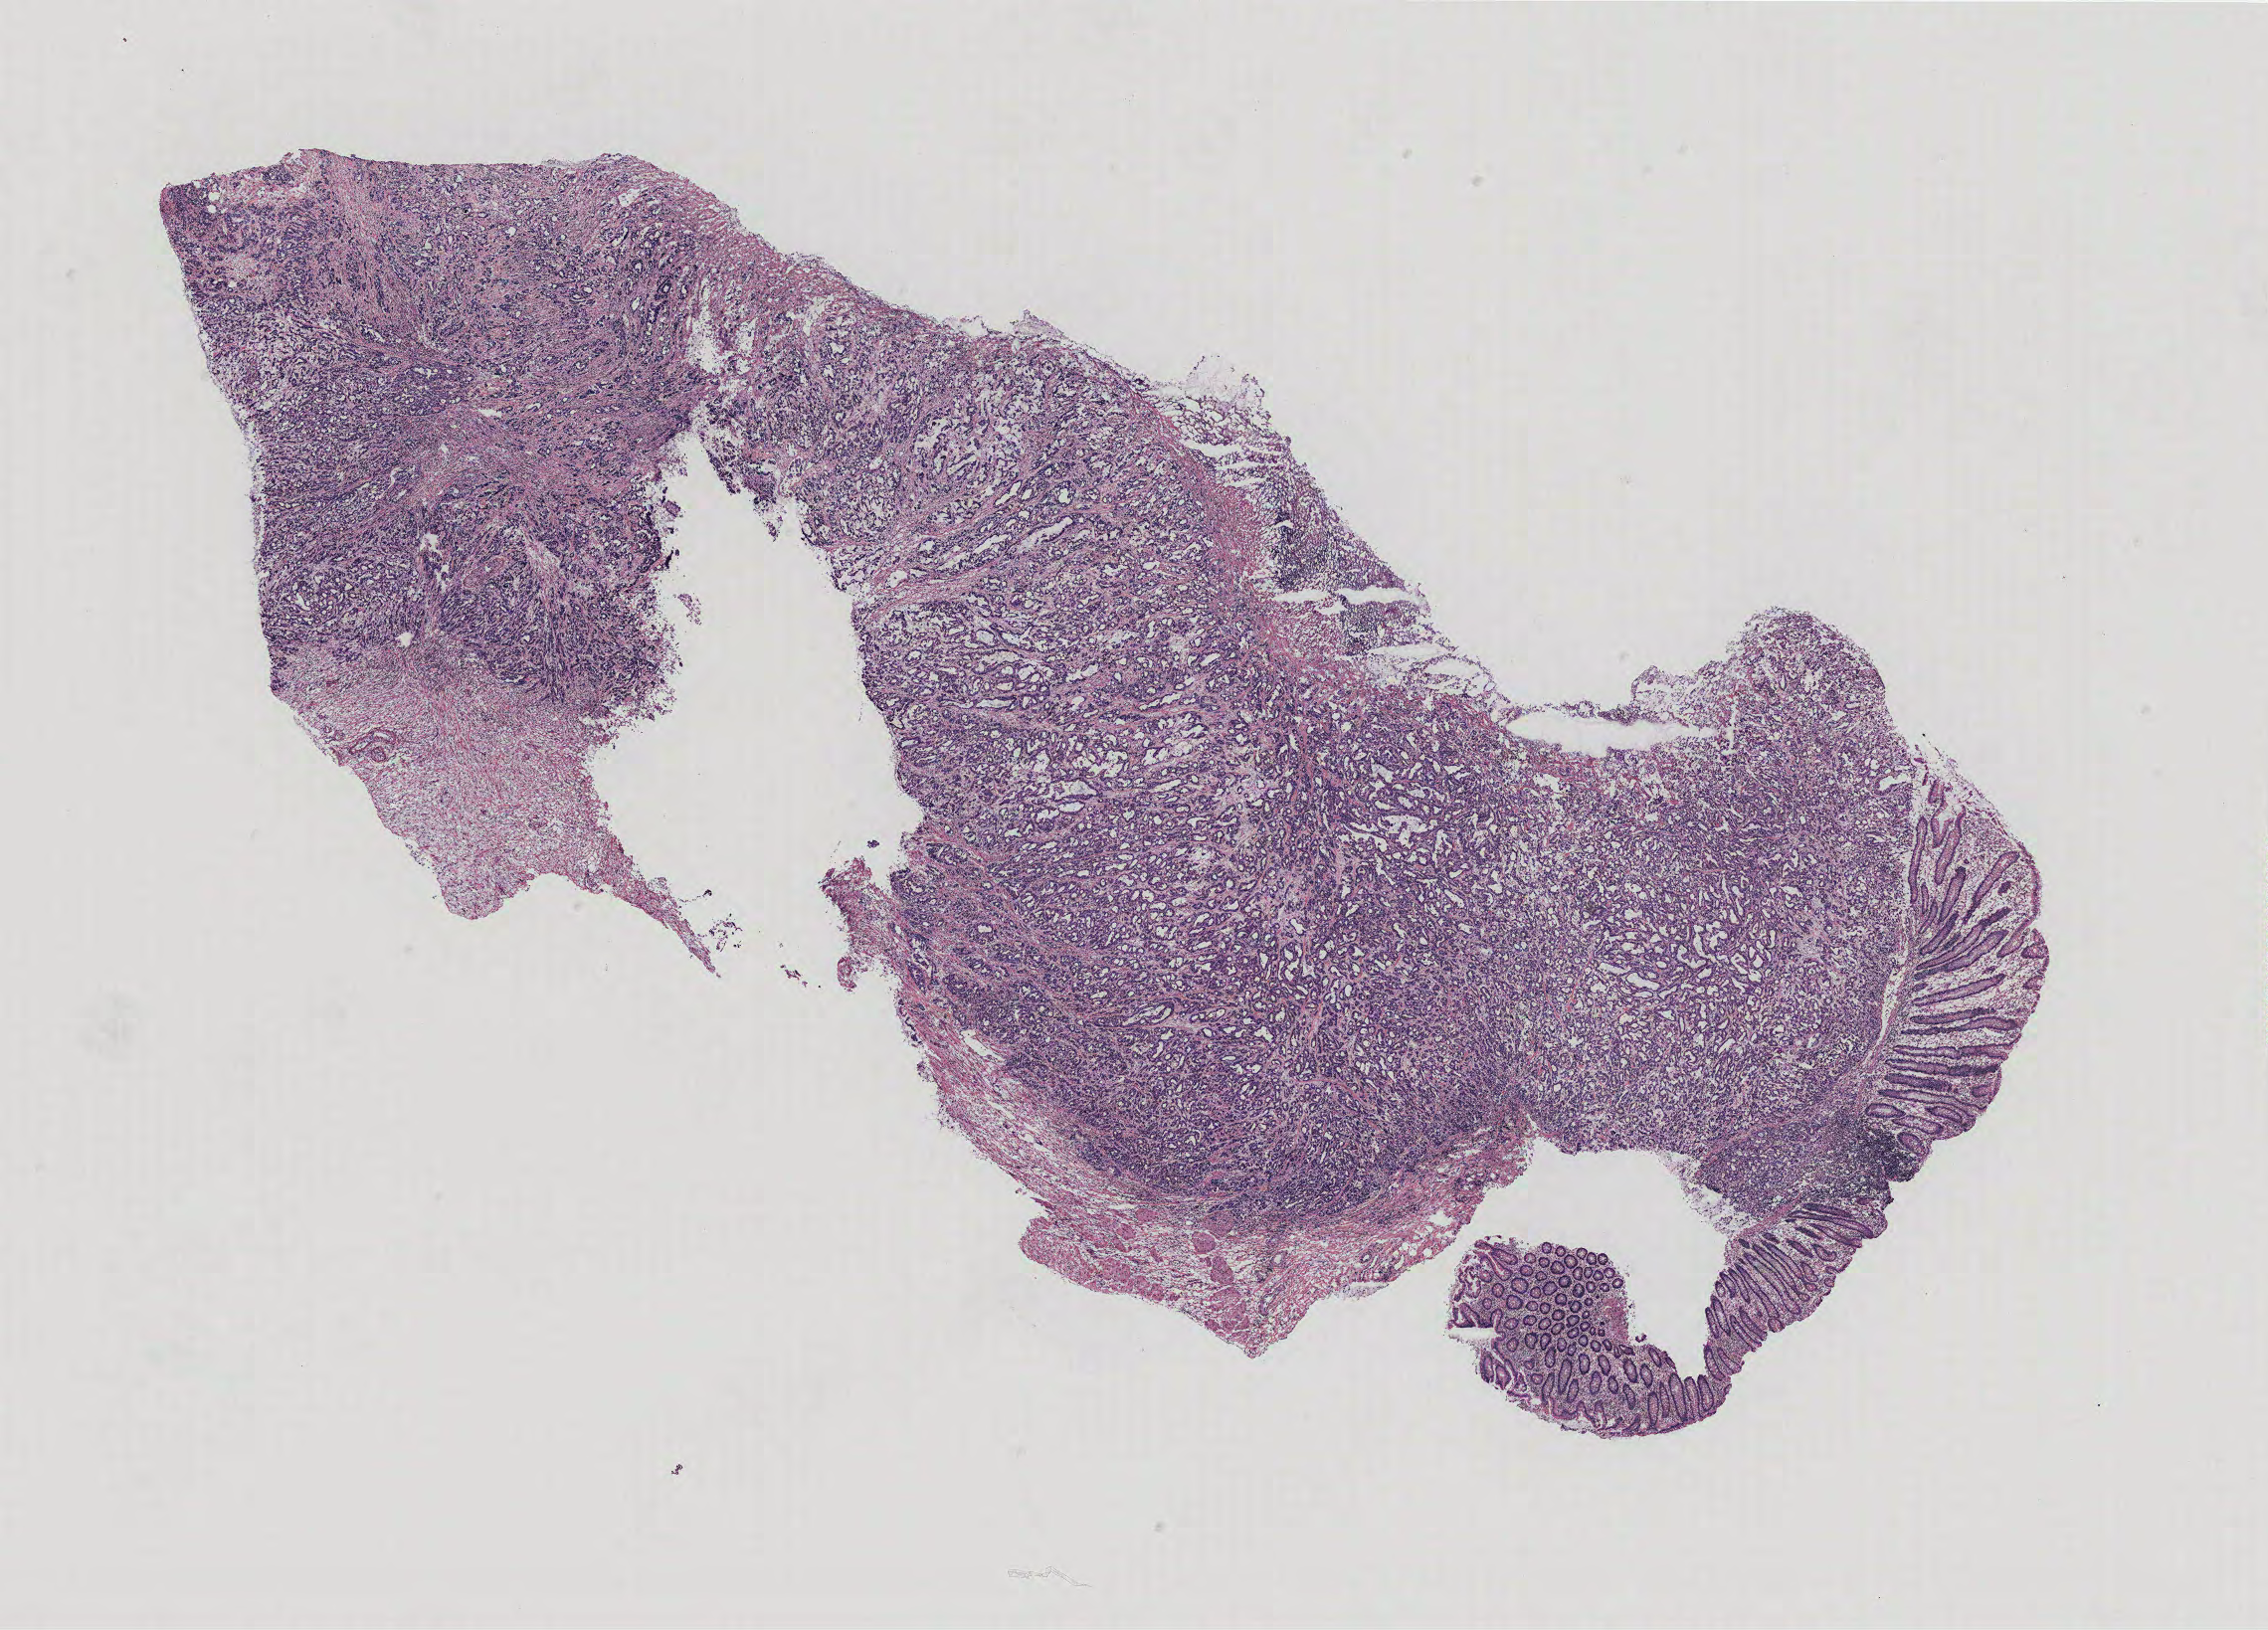
H&E whole-slide image — shown as a low-resolution overview of the whole scanned area (about 18.2 x 13.1 mm, from a 40x scan), tumour tissue sample, colon. 78-year-old female patient.
• primary tumour site (as recorded): colon
• histologic diagnosis: Adenocarcinoma, NOS
• AJCC pathologic stage: IIIC